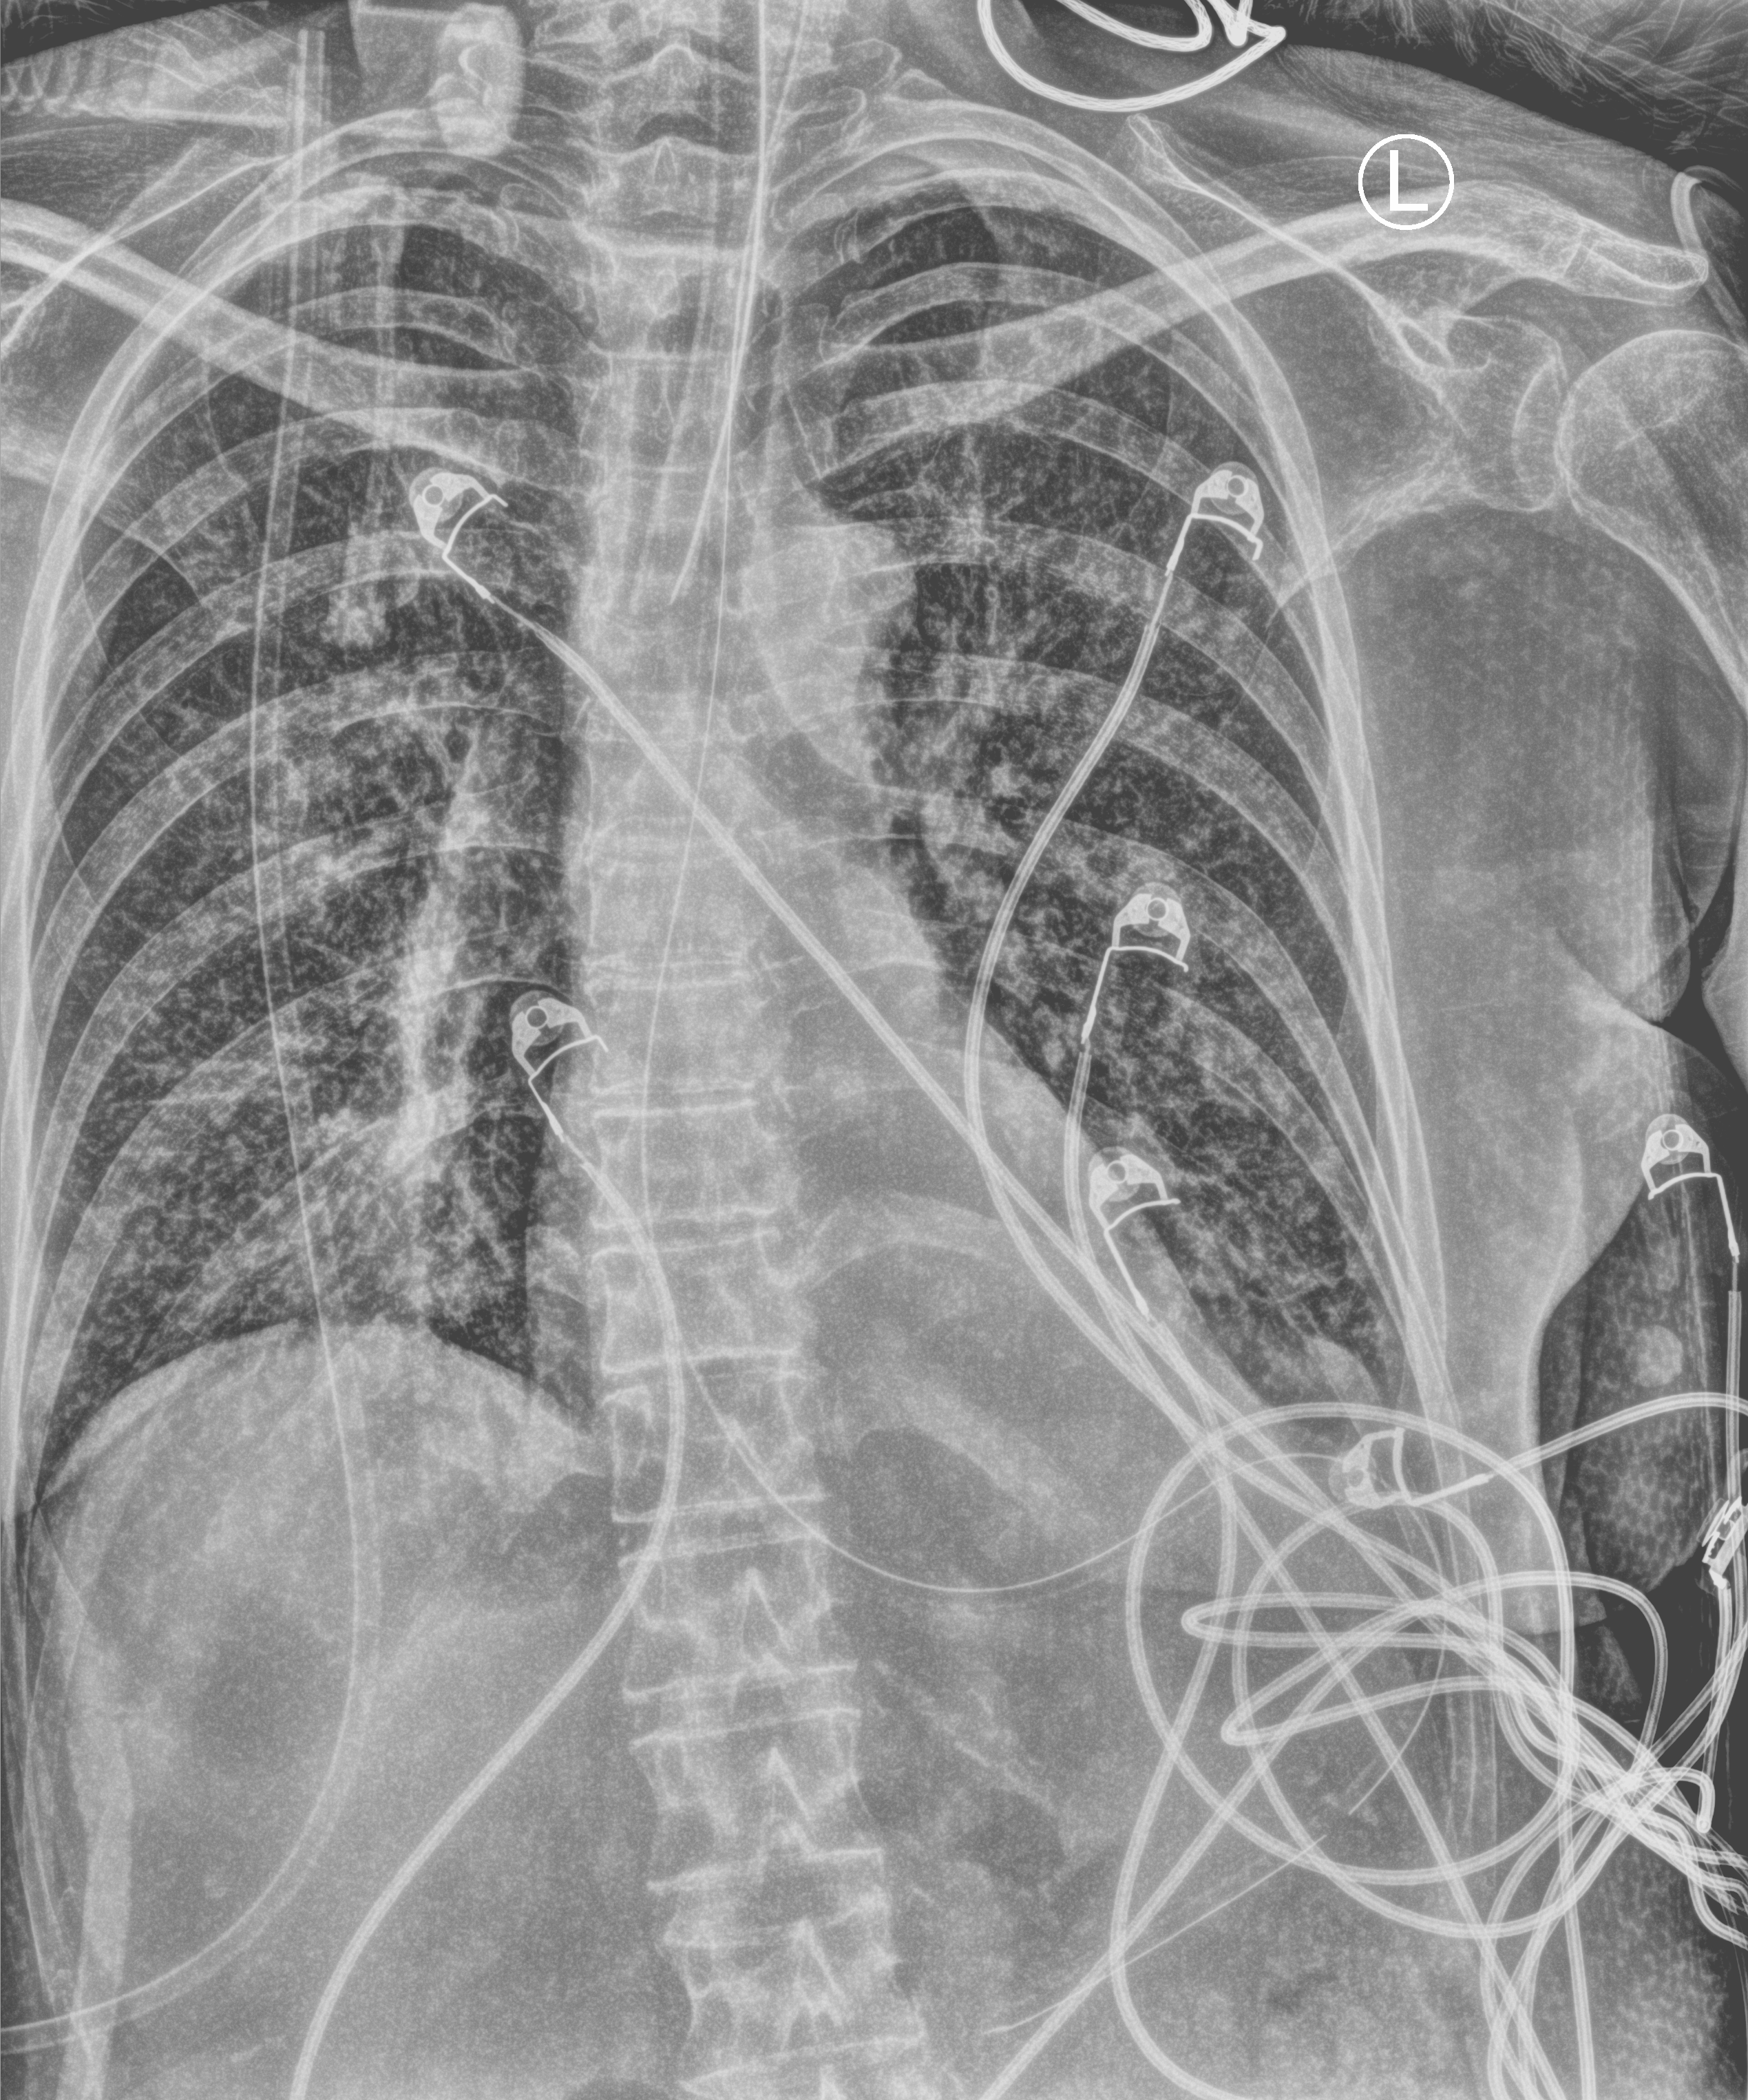
Chest X-ray (portable). Patient hospitalised with COVID-19, aged 18–59 years.
From the hospital-stay record, not from the radiograph (when in the stay this image was taken is not recorded): smoking status (admission record): never; length of hospital stay: 11 days; admitted to intensive care during this hospital stay: yes.